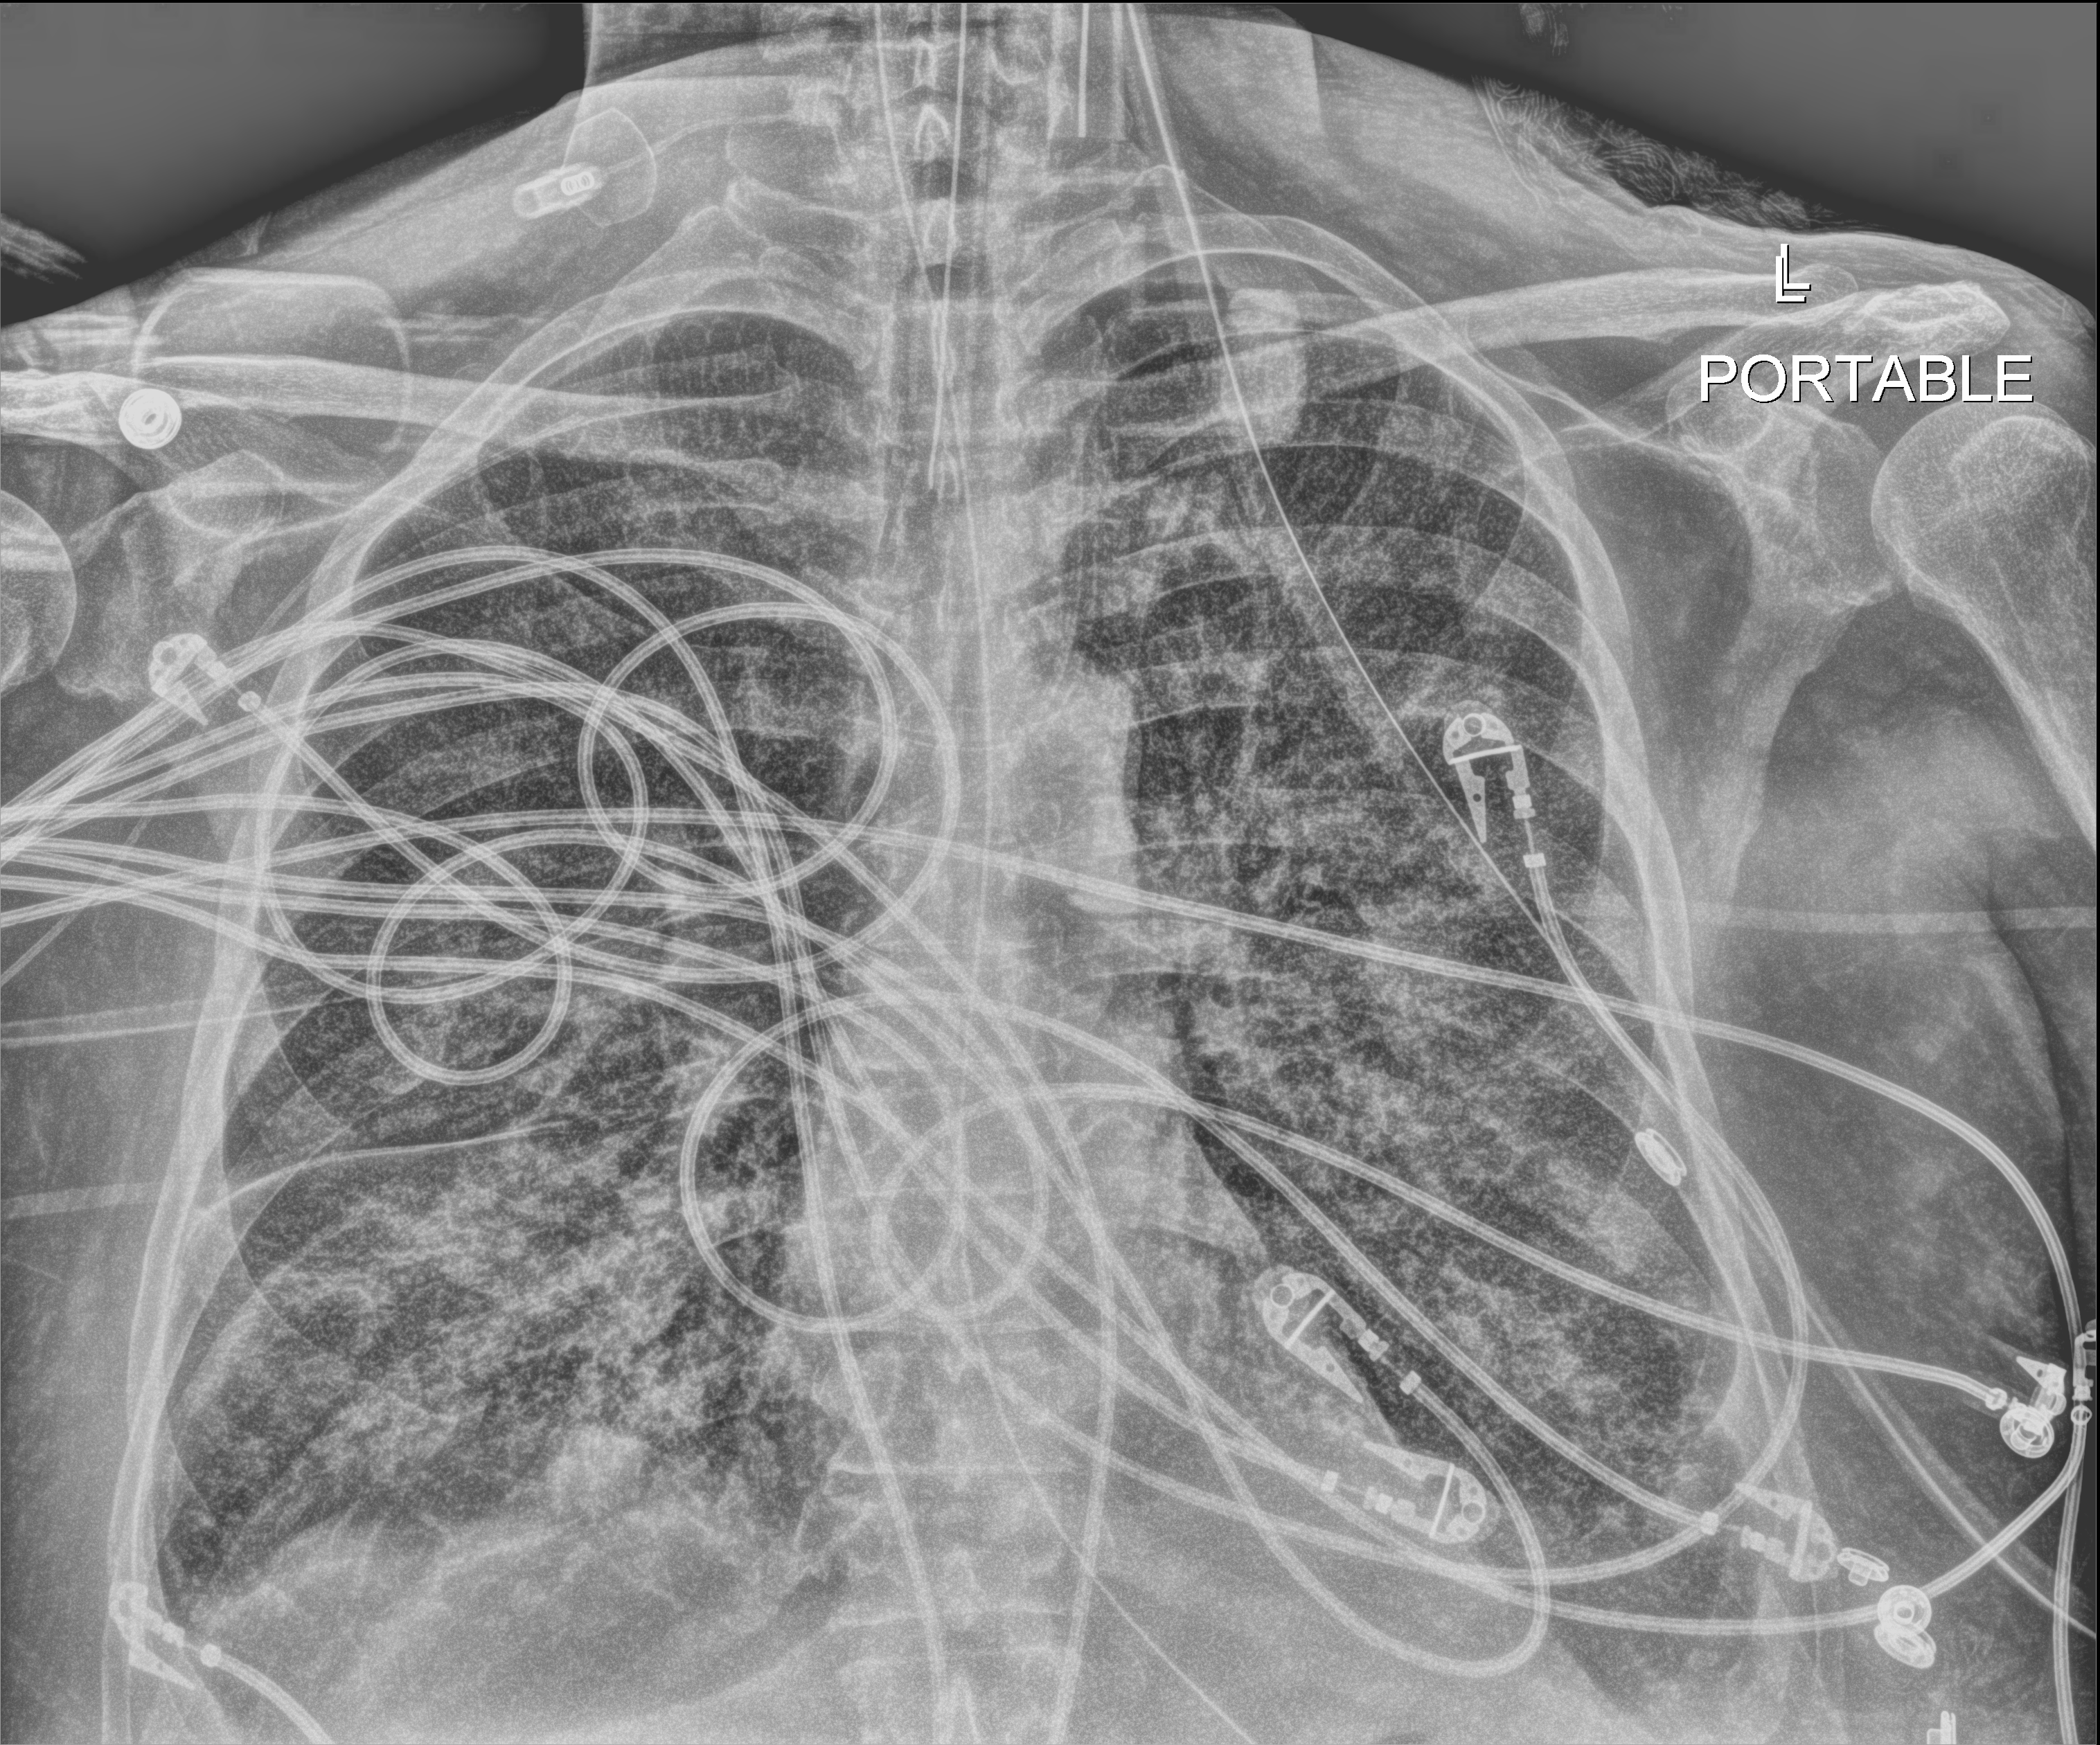
Chest X-ray (portable); anteroposterior (AP) projection. Male patient hospitalised with COVID-19, age 60–74 years.
Hospital-stay facts (about this admission, not read from this image; timing relative to this image not recorded): admitted to intensive care during this hospital stay: yes.